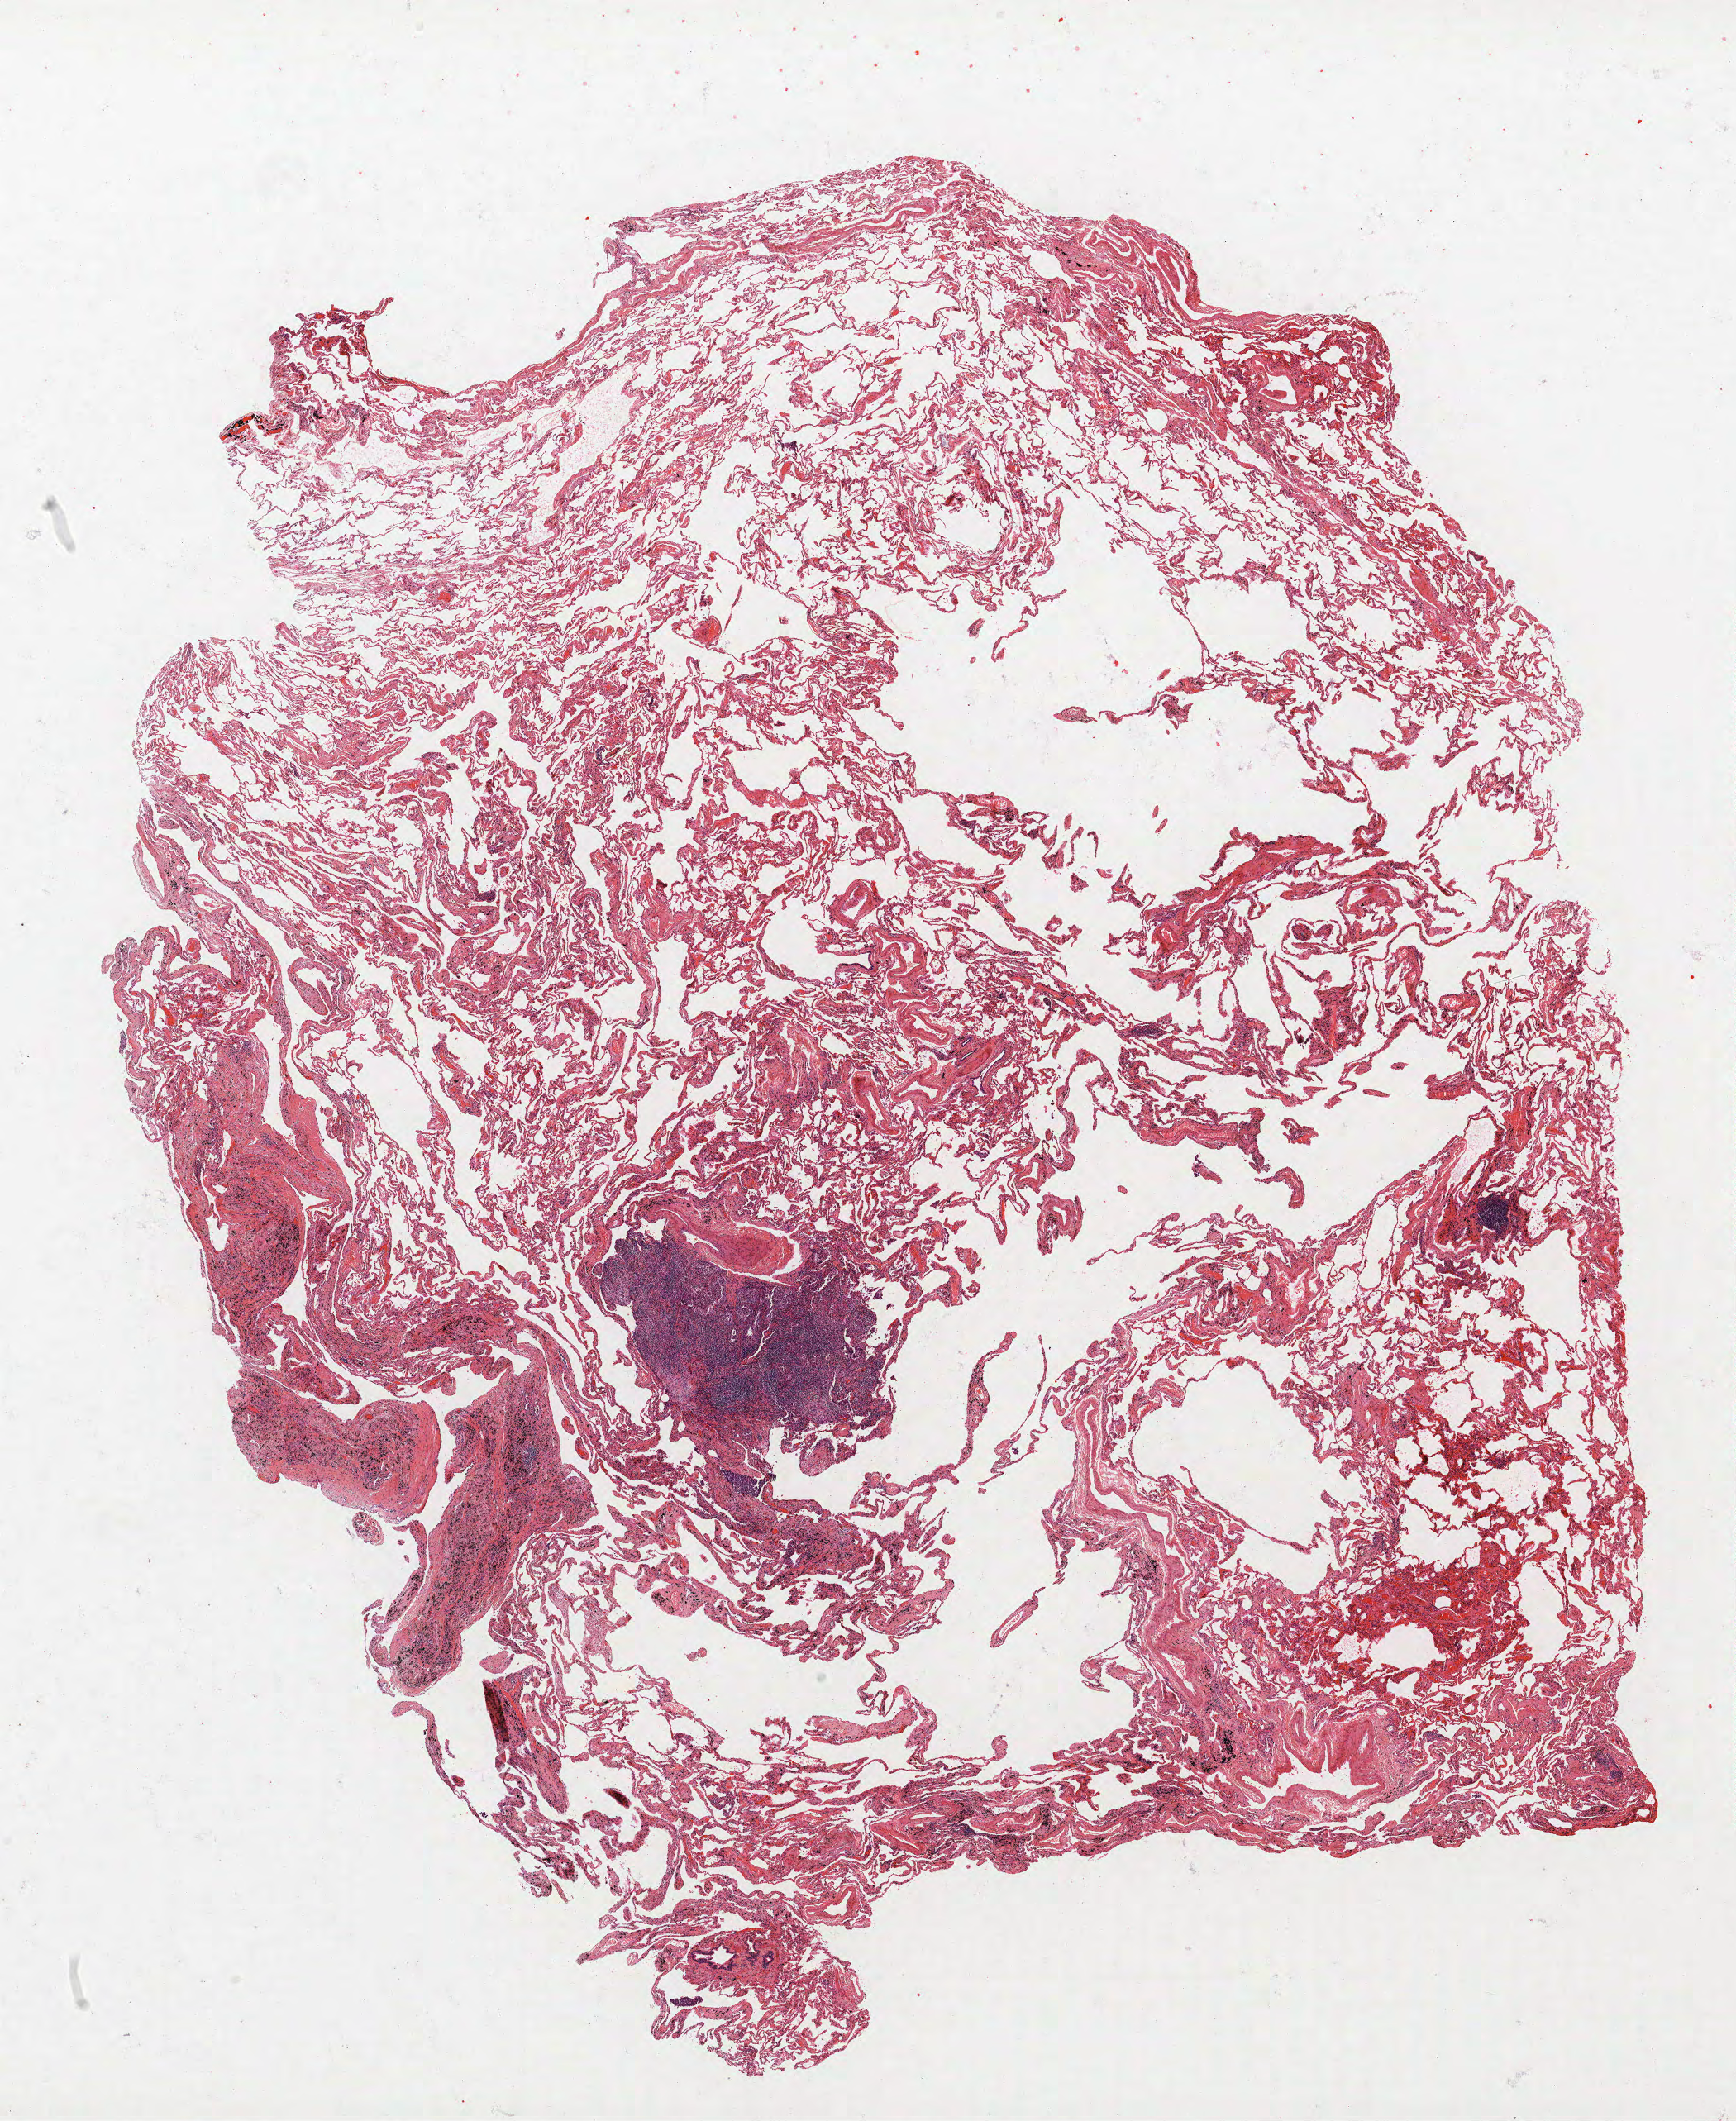
Whole-slide histology image, H&E-stained, whole scanned area (about 16.8 x 20.5 mm) shown as a low-resolution overview. Formalin-fixed paraffin-embedded (FFPE) section. Lung tissue. Male patient, aged 74 at enrolment. Former smoker at enrolment. Grade: poorly differentiated (G3).
Participant's lung-cancer diagnosis: Adenocarcinoma, NOS. Tumour size (pathology): 6 mm. Primary tumour location (clinical record): right upper lobe. Stage (AJCC 6th edition): IA.